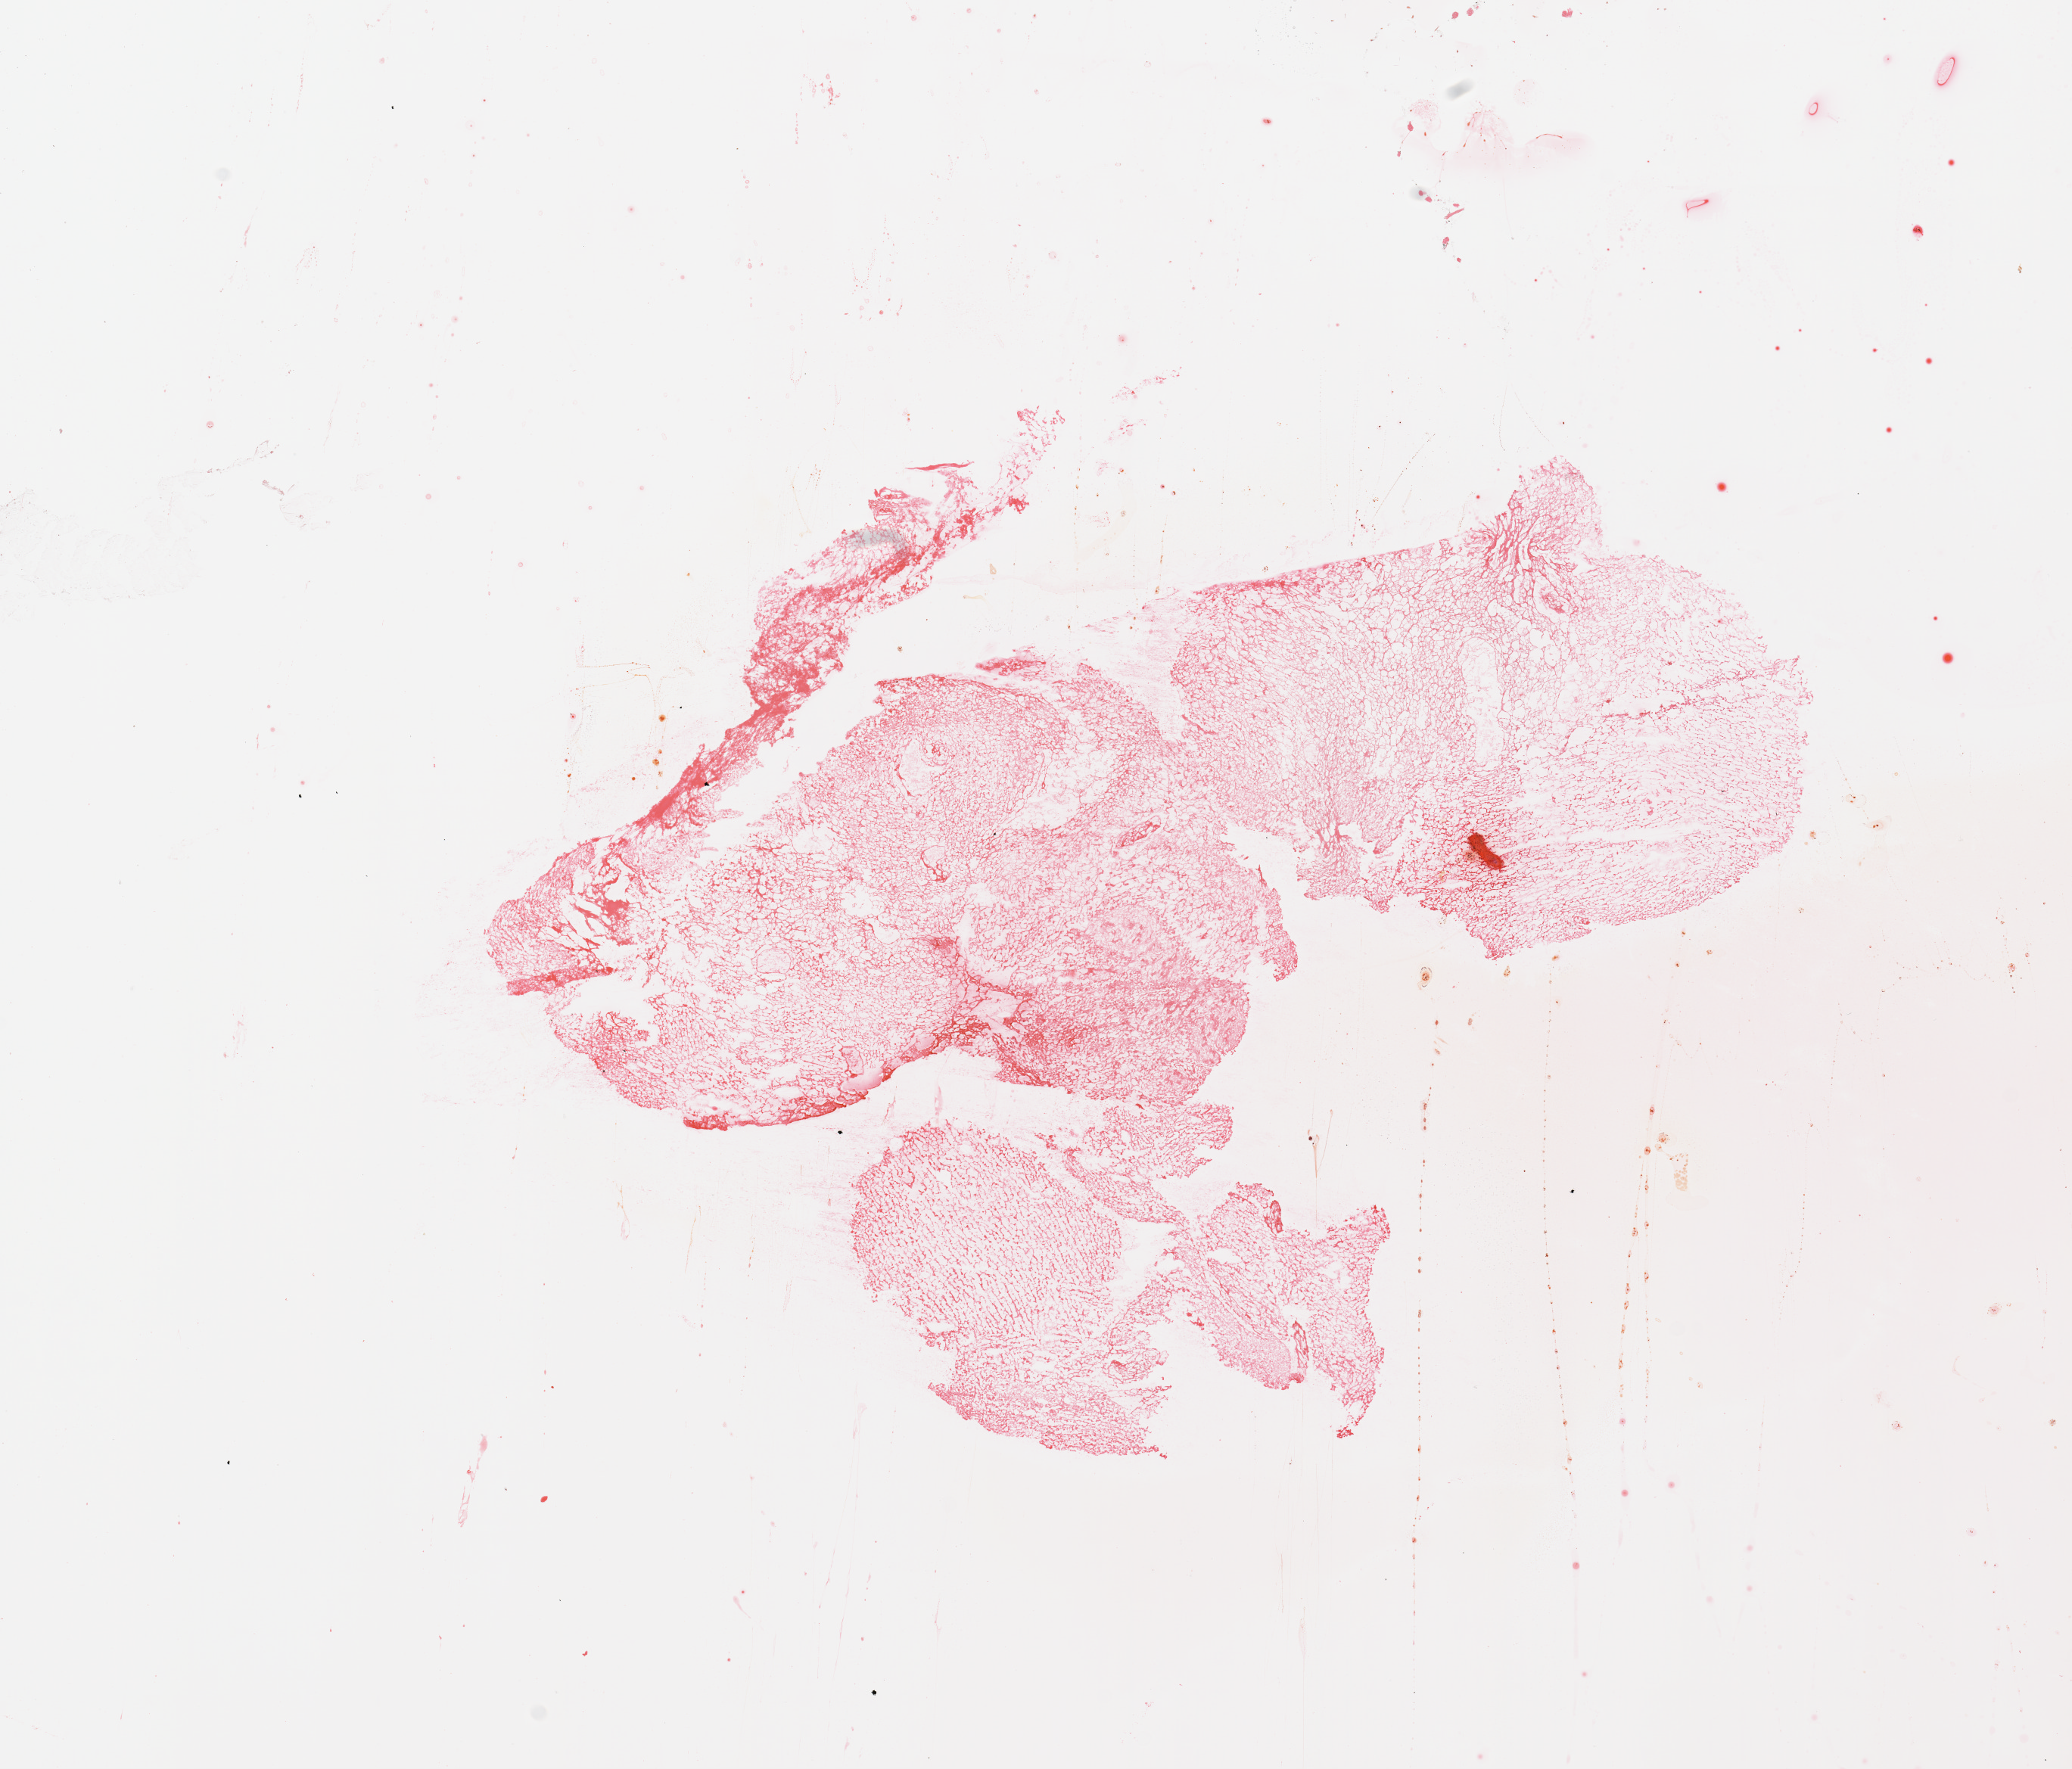
Whole-slide histology image, H&E — whole scanned area (about 10.8 x 9.2 mm) shown as a low-resolution overview, brain, tumour tissue. Patient: male, age 68 years.
- patient diagnosis (cohort enrolment): glioblastoma multiforme (brain)
- primary tumour site (as recorded): occipital lobe